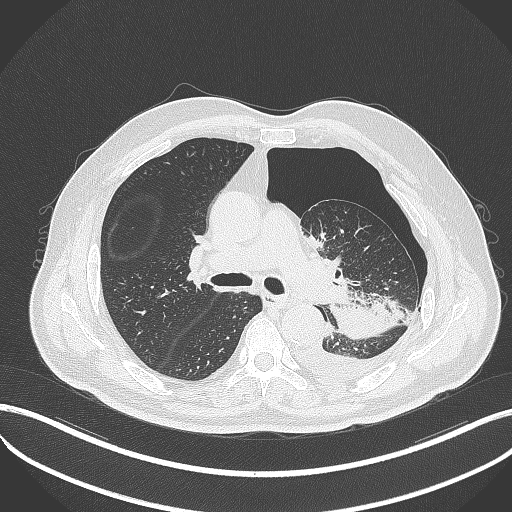
Chest CT, one axial slice. Position 319 of 464 along the scan axis. Lung window (W 1500 / L -600 HU). 1 mm slice thickness. 512 × 512 image matrix, field of view 400 × 400 mm. Patient: male, 76 years. From the clinical record (not read from this slice): clinical TNM (as recorded): T3 N0 M1b.
Outlined on this slice (rectangle marked by the reading radiologist):
- lung tumour (recorded histology: adenocarcinoma): bounding box [x1, y1, x2, y2] px = [324, 293, 396, 340]